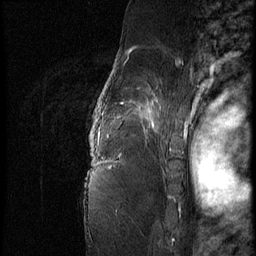
Breast MRI (dynamic contrast-enhanced), one sagittal slice. Position 57 of 62 along the scan axis. 3 images stored at this slice position (order not interpretable as contrast timing). 1.5 T. TE 4.2 ms, TR 9 ms. 2.5 mm slice thickness. 256 × 256 image matrix, field of view 180 × 180 mm. Female patient, age 56 years. Case-level facts recorded for this patient, not image findings: setting: breast cancer imaged before/during neoadjuvant chemotherapy; receptor status: HER2-positive.
Annotated regions visible in this slice (semi-automatic segmentation, software-assisted and operator-edited):
- analysis volume of interest (the breast-tissue region the enhancement analysis was run in; not a lesion): bounding box [x1, y1, x2, y2] px = [84, 75, 181, 153]
- tumour enhancement mask (voxels above the 140 % enhancement threshold inside the analysis volume of interest): [96, 86, 158, 133]